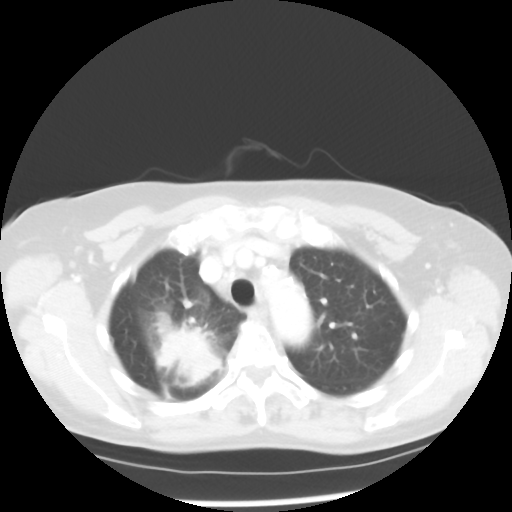
Chest CT, one axial slice. Reconstruction kernel STANDARD. Lung window (W 1500 / L -600 HU). 5 mm slice thickness. 512 × 512 image matrix. Patient: female, 60 years. From the clinical record (not read from this slice): clinical TNM (as recorded): T2 N1 M1a.
Structures marked on this image (rectangle marked by the reading radiologist):
- lung tumour (recorded histology: adenocarcinoma): bounding box (x1, y1, x2, y2) in pixels: (151, 318, 224, 392)